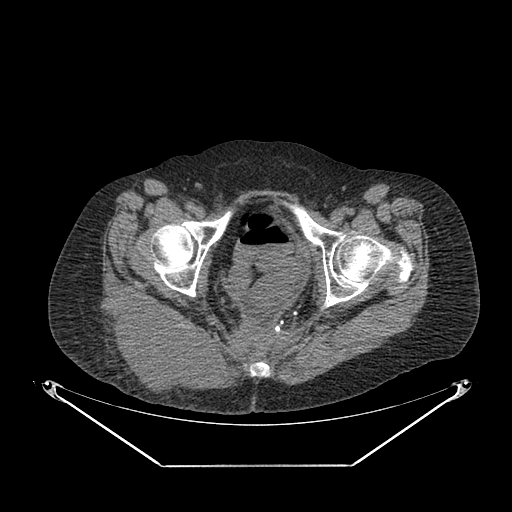
CT of an extremity soft-tissue mass (from a PET/CT study), one axial slice. Position 54 of 267 along the scan axis. Reconstruction kernel SOFT. 140 kVp. Soft-tissue window (W 400 / L 40 HU). 512 × 512 image matrix, field of view 500 × 500 mm. Female patient. From the clinical record (not read from this slice): histological type: spindle cell suggestive of myxofibrosarcoma; grade: intermediate; site of the primary tumour: right buttock.
Outlined on this slice (expert contour drawn on MRI and transferred to this co-registered scan by the dataset authors):
- gross tumour volume (mass): bounding box <110,299,216,396> (left, top, right, bottom; pixels)